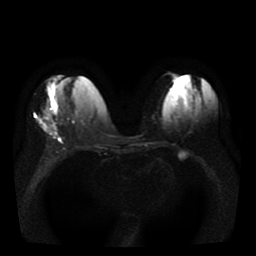
Breast MRI, one axial slice; position 15 of 41 along the scan axis; diffusion-weighted series; image 2 of 4 stored at this slice position (different b-values; order by instance number); 1.5 T; 256 × 256 image matrix, field of view 330 × 330 mm. Female patient.
Outlined on this slice (outlined manually by an expert reader):
- tumour on diffusion-weighted imaging: box from (x=38, y=116) to (x=59, y=136) px